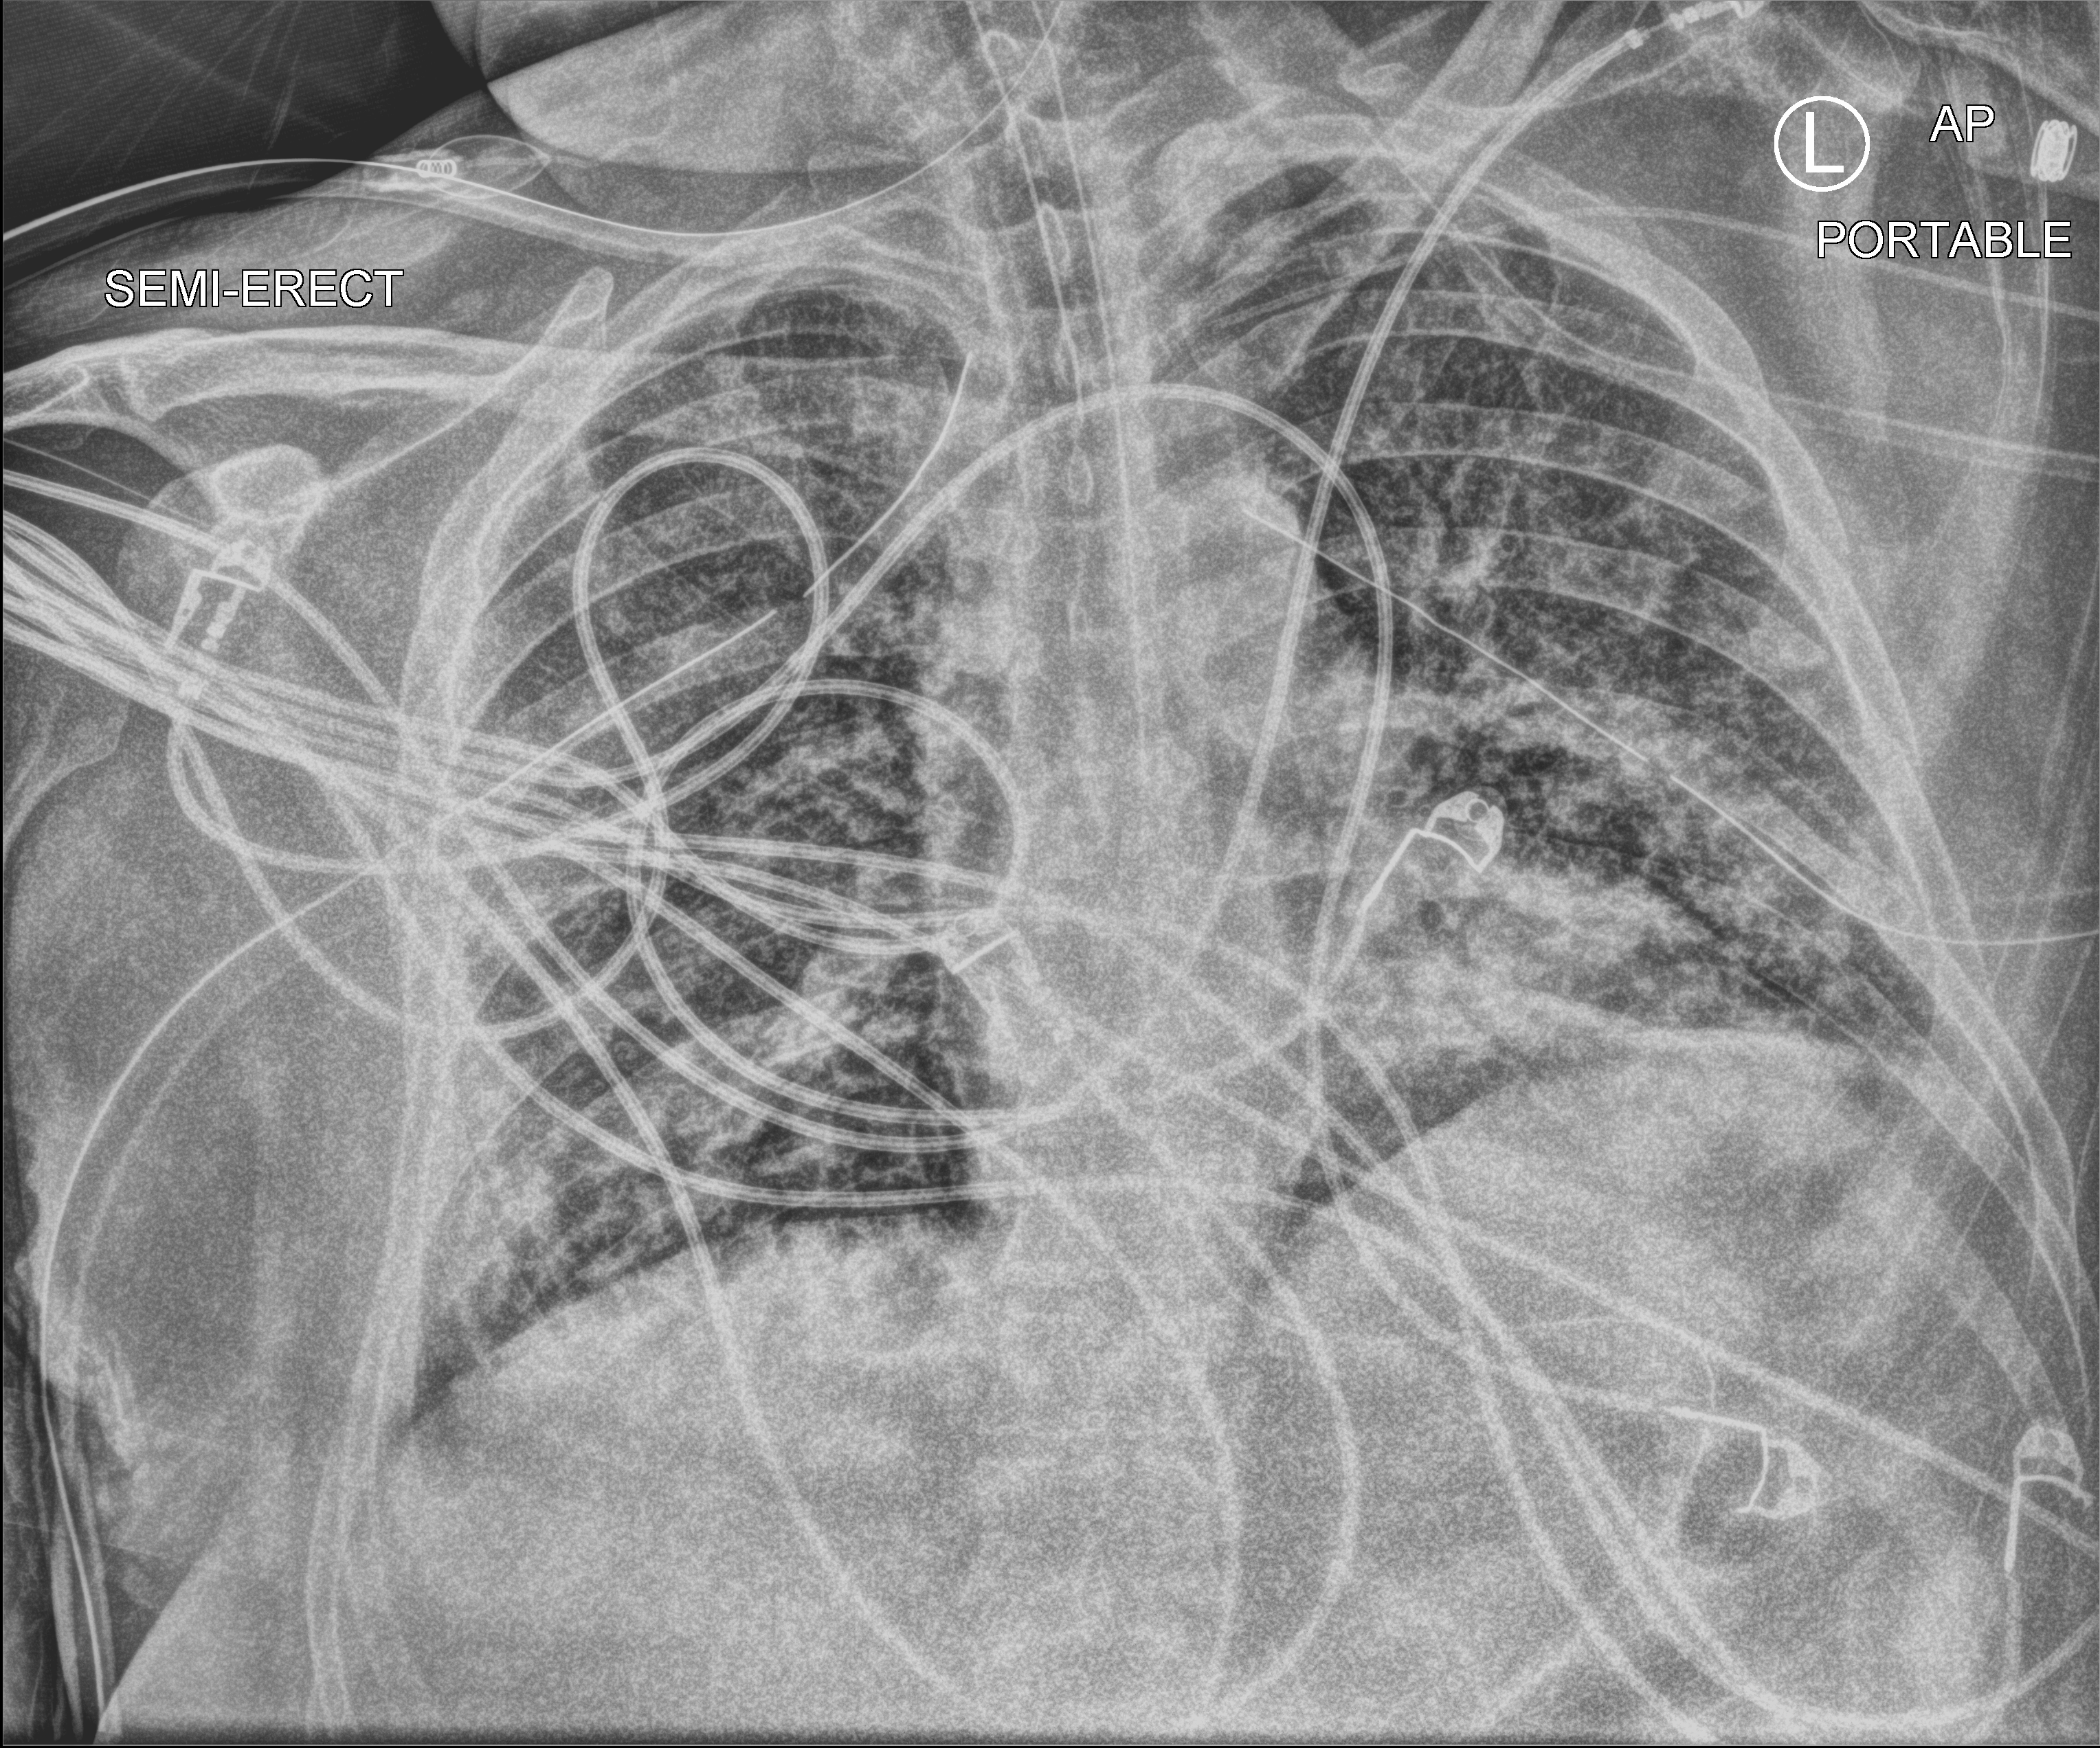
Portable chest radiograph; anteroposterior (AP) projection. Male patient hospitalised with COVID-19, age 18–59 years.
From the hospital-stay record, not from the radiograph (when in the stay this image was taken is not recorded):
- chronic kidney disease (admission record): no
- admitted to intensive care during this hospital stay: yes